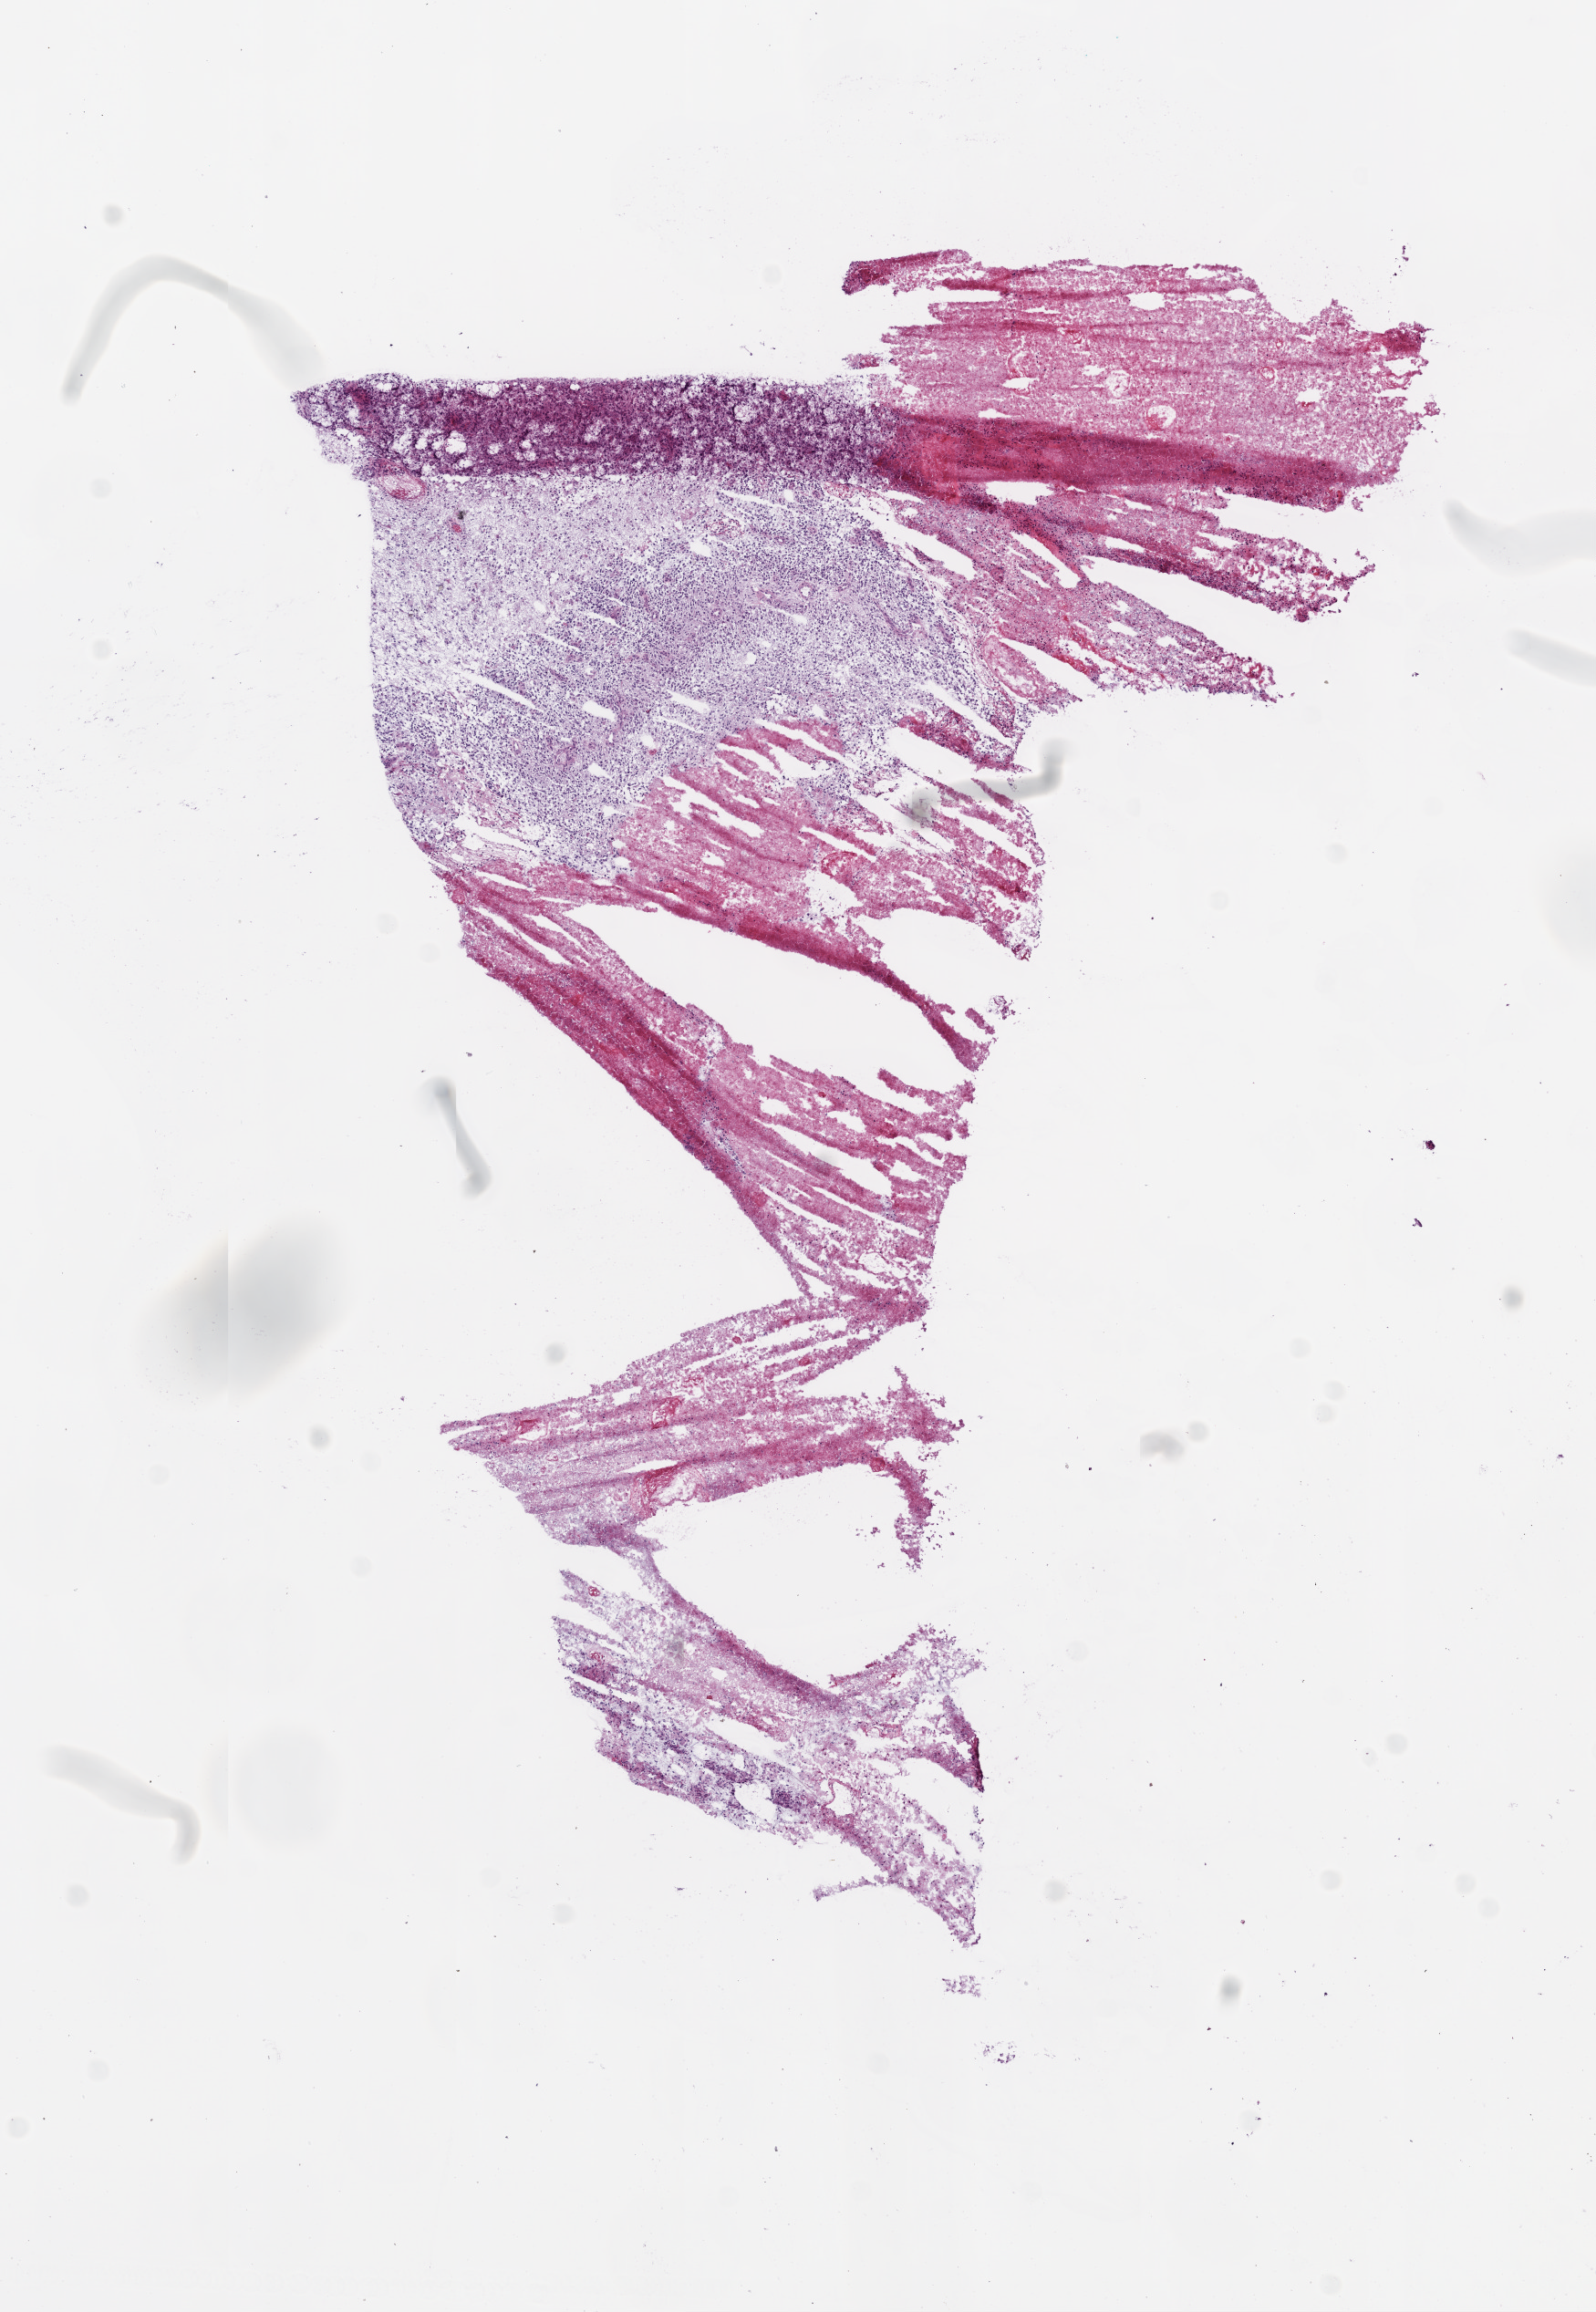
H&E whole-slide image — low-resolution overview of the scanned area, about 7.0 x 10.2 mm (from a 20x scan), frozen section from the bottom of the tissue portion, sample: primary tumour, brain. Patient: female, age at initial diagnosis 81 years. Pathologist review of this section (percent, as recorded): tumour cells 40%, tumour nuclei 80%, normal cells 0%, stromal cells 0%, necrosis 60%.
Diagnosis: Glioblastoma.